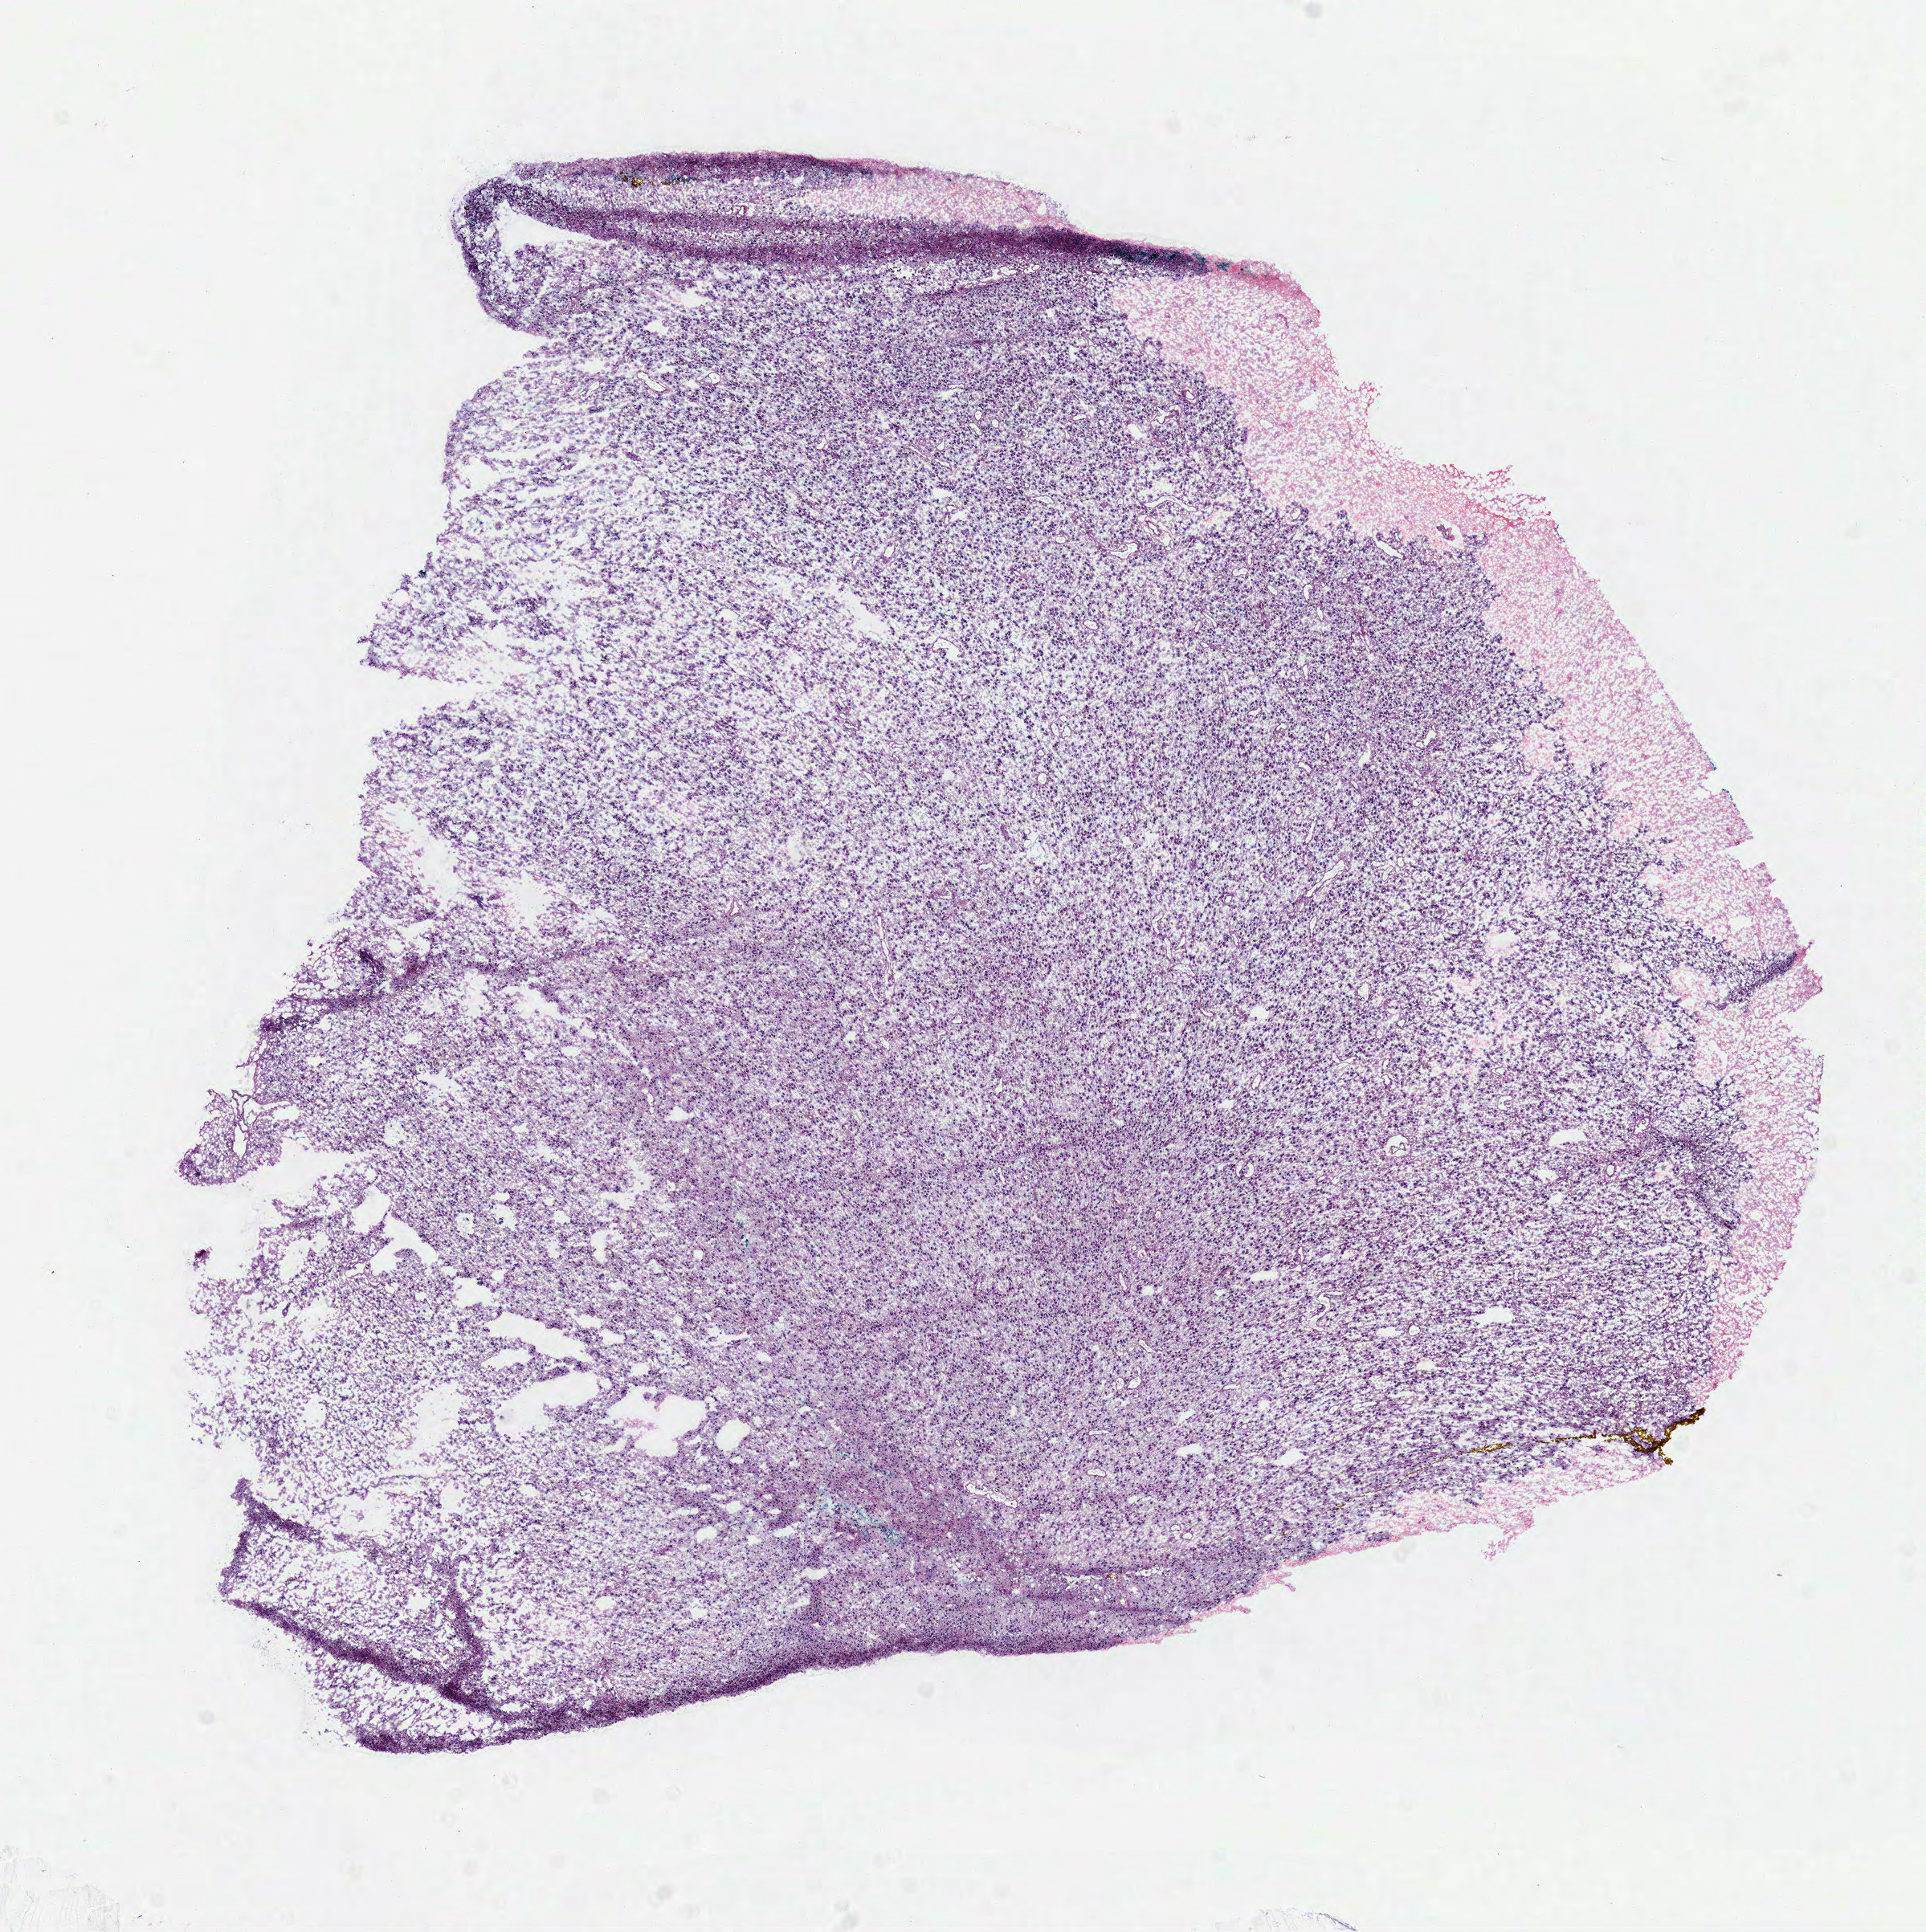
H&E whole-slide image, shown as a low-resolution overview of the whole scanned area (about 9.7 x 9.7 mm, slide scanned at 40x); frozen section from the top of the tissue portion; primary tumour sample from the brain. Male patient; age at initial diagnosis 39 years. Histologic grade: G3 (poorly differentiated). Composition of this section per pathologist review: tumour cells 100%, tumour nuclei 85%, normal cells 0%, stromal cells 0%, necrosis 0%.
• histologic diagnosis: Astrocytoma, anaplastic (cerebrum)
• laterality: left